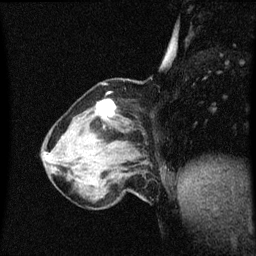
Breast MRI (dynamic contrast-enhanced), one sagittal slice. Slice 16 of 60 in the series (ordered by position). Dynamic contrast-enhanced series, image 2 of 3 at this slice position (ordered by acquisition). 1.5 T. TE 4.2 ms, TR 8.4 ms. 2 mm slice thickness. 256 × 256 image matrix, field of view 200 × 200 mm. Patient: female, 64 years. Case-level facts recorded for this patient, not image findings: setting: breast cancer imaged before/during neoadjuvant chemotherapy; receptor status: HR-positive, HER2-negative.
Outlined on this slice (semi-automatic segmentation, software-assisted and operator-edited):
- analysis volume of interest (the breast-tissue region the enhancement analysis was run in; not a lesion): bounding box [x1, y1, x2, y2] px = [58, 100, 143, 167]
- tumour enhancement mask (voxels above the 70 % enhancement threshold inside the analysis volume of interest): [98, 100, 115, 117]